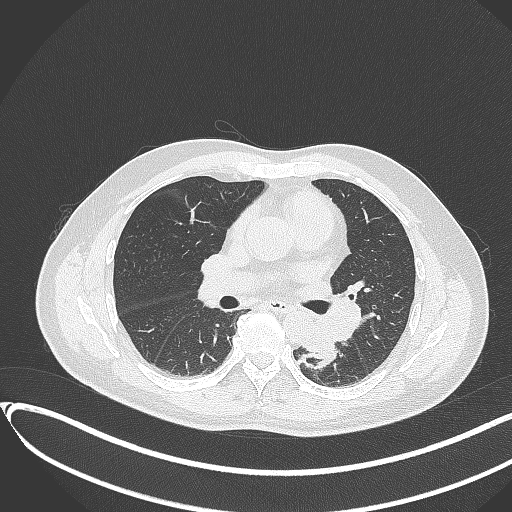
Chest CT, one axial slice. Slice 187 of 417 in the series (ordered by position). Reconstruction kernel B70f. 120 kVp. Lung window (W 1500 / L -600 HU). 1 mm slice thickness. 512 × 512 image matrix. Male patient, age 54 years. From the clinical record (not read from this slice): clinical TNM (as recorded): T3 N0 M0.
Outlined on this slice (rectangle marked by the reading radiologist):
- lung tumour (recorded histology: squamous cell carcinoma): box from (x=300, y=320) to (x=345, y=370) px